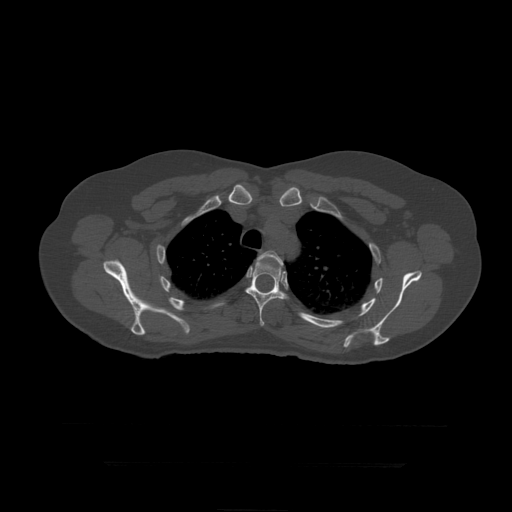
CT including the spine, one axial slice. Position 337 of 399 along the scan axis. Reconstruction kernel STANDARD. Bone window (W 1800 / L 400 HU). 1.25 mm slice thickness. 512 × 512 image matrix, field of view 450 × 450 mm. Patient age 41 years. From the clinical record (not read from this slice): primary cancer: breast.
Outlined on this slice (semi-automatic segmentation, software-assisted and operator-edited):
- T4 vertebra: bounding box (x1, y1, x2, y2) in pixels: (255, 251, 284, 272)
- T5 vertebra: (245, 255, 289, 326)